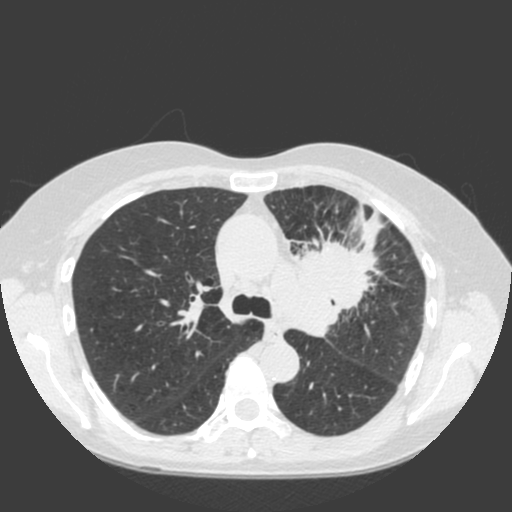
Low-dose screening chest CT, one axial slice. Position 127 of 184 along the scan axis. Lung window (W 1500 / L -600 HU). 2 mm slice thickness. 512 × 512 image matrix.
Outlined on this slice (outlined manually by an expert reader):
- lesion 1 (tumor, hilum of left lung): box from (x=287, y=201) to (x=382, y=337) px